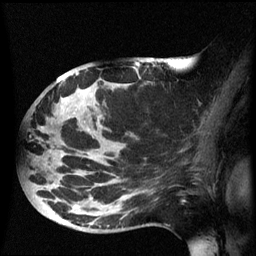
Breast MRI (dynamic contrast-enhanced), one sagittal slice. Position 34 of 60 along the scan axis. Dynamic contrast-enhanced series, image 2 of 3 at this slice position (ordered by acquisition). 1.5 T. TE 4.2 ms, TR 8.4 ms. 2.5 mm slice thickness. 256 × 256 image matrix, field of view 220 × 220 mm. Female patient, age 49 years.
Annotated regions visible in this slice (semi-automatically segmented with operator editing):
- analysis volume of interest (the breast-tissue region the enhancement analysis was run in; not a lesion): bounding box [x1, y1, x2, y2] px = [24, 72, 183, 233]
- tumour enhancement mask (voxels above the 70 % enhancement threshold inside the analysis volume of interest): [77, 72, 79, 75]